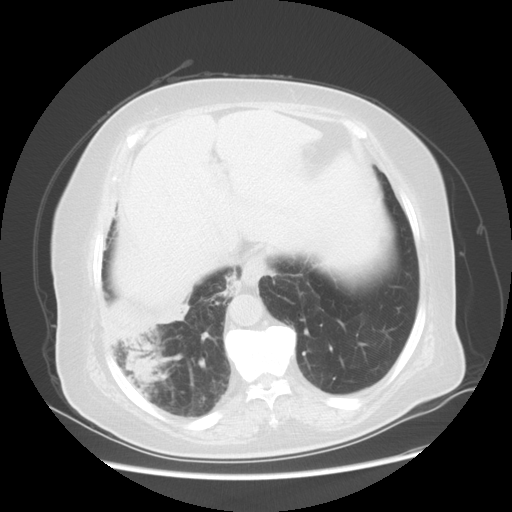
Chest CT, one axial slice. Slice 13 of 56 in the series (ordered by position). Lung window (W 1500 / L -600 HU). 512 × 512 image matrix, field of view 378 × 378 mm. Patient: female, 73 years. From the clinical record (not read from this slice): clinical TNM (as recorded): T3 N0 M0.
Annotated regions visible in this slice (bounding box drawn by a radiologist):
- lung tumour (recorded histology: adenocarcinoma): bounding box <101,325,177,394> (left, top, right, bottom; pixels)